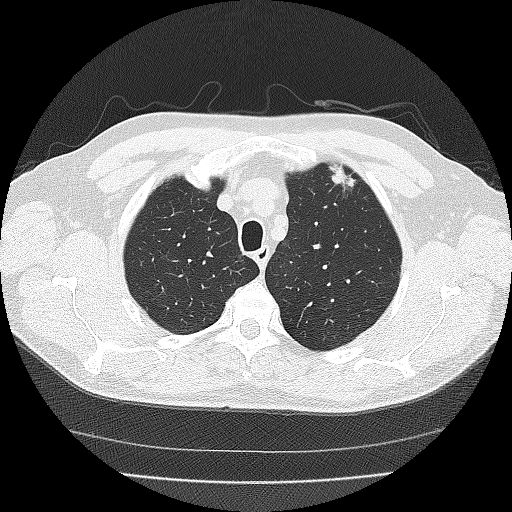
Low-dose screening chest CT, one axial slice; slice 133 of 167 in the series (ordered by position); 120 kVp; lung window (W 1500 / L -600 HU); 2 mm slice thickness; 512 × 512 image matrix, field of view 359 × 359 mm.
Outlined on this slice (expert manual segmentation):
- lesion 1 (tumor, upper lobe of left lung): box from (x=329, y=162) to (x=356, y=187) px